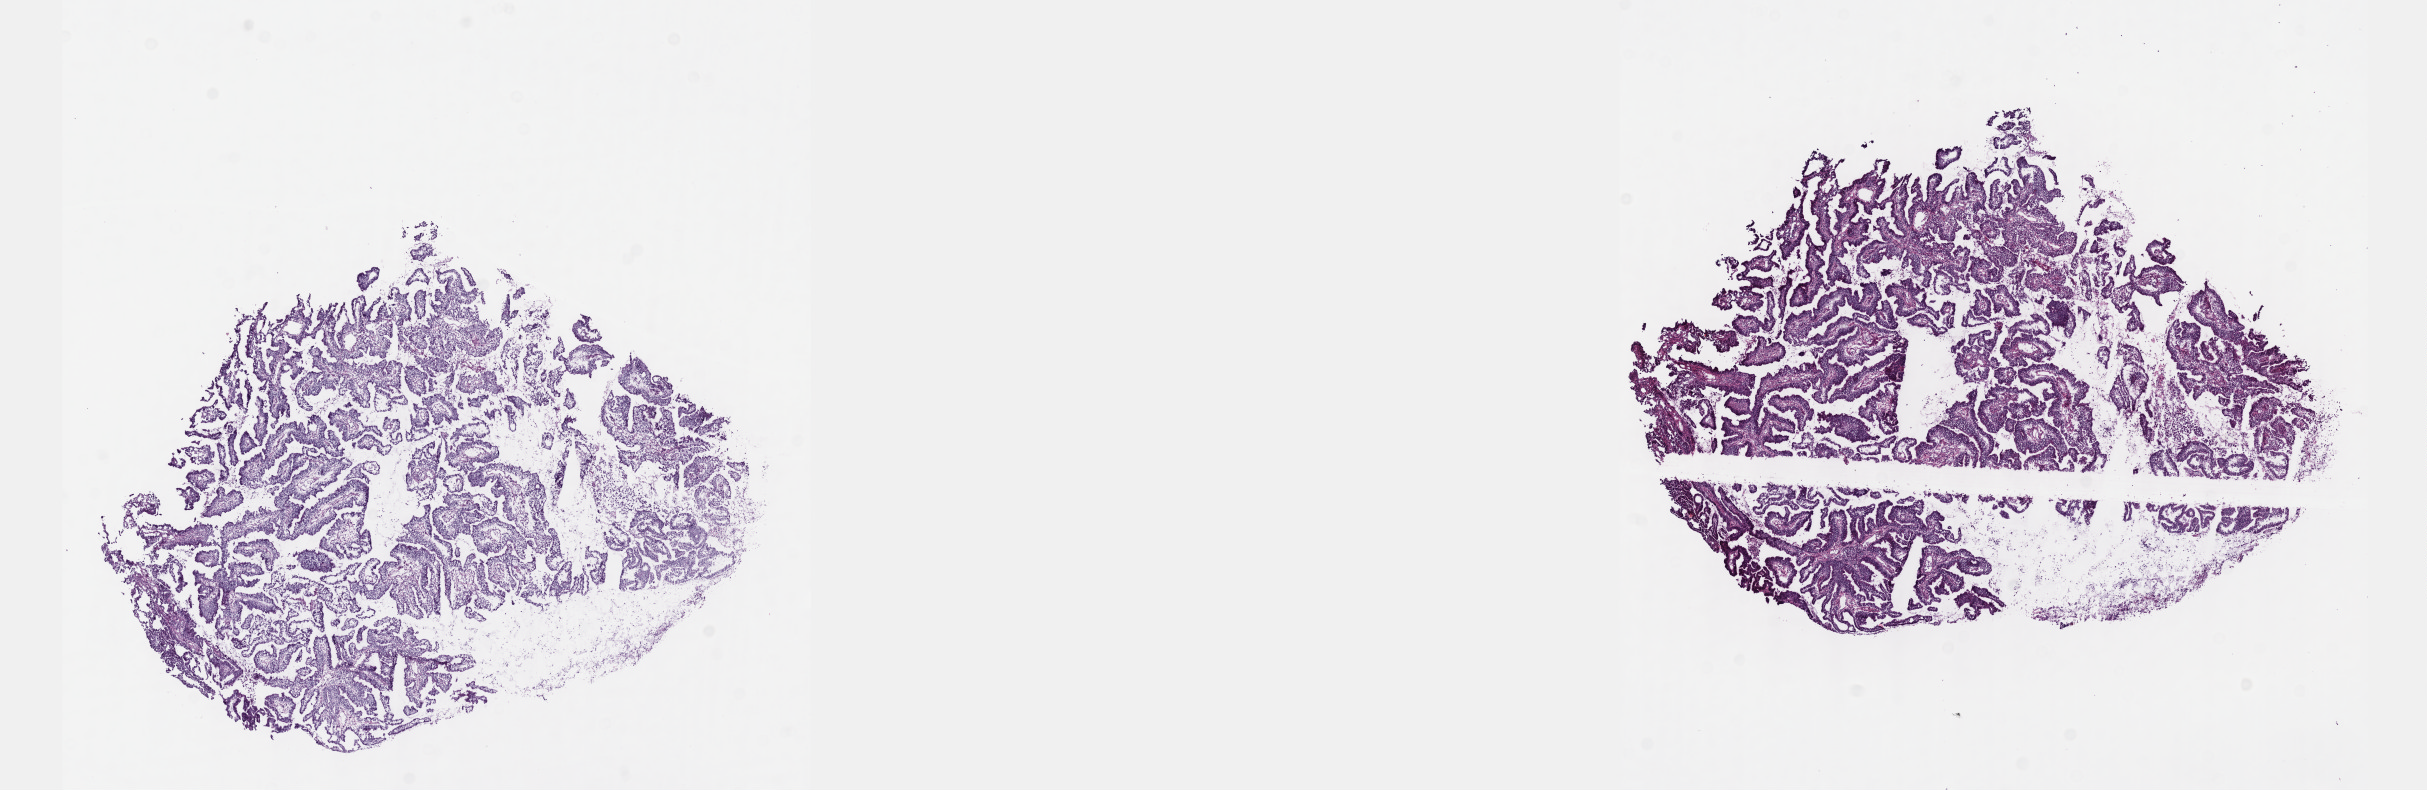
Whole-slide histology image, H&E-stained — a low-resolution overview of the entire scanned area, about 19.6 x 6.4 mm (slide scanned at 40x); frozen section from the top of the tissue portion; sample: primary tumour, cervix. Female patient; age at initial diagnosis 43 years. Histologic grade: G2 (moderately differentiated). Slide review estimates, as recorded: tumour cells 70%, tumour nuclei 70%, normal cells 10%, stromal cells 20%, necrosis 0%. Infiltration values recorded for this section: lymphocyte infiltration 5%, monocyte infiltration 5%, neutrophil infiltration 5%.
FIGO stage: IIB. Diagnosis: Mucinous adenocarcinoma, endocervical type.